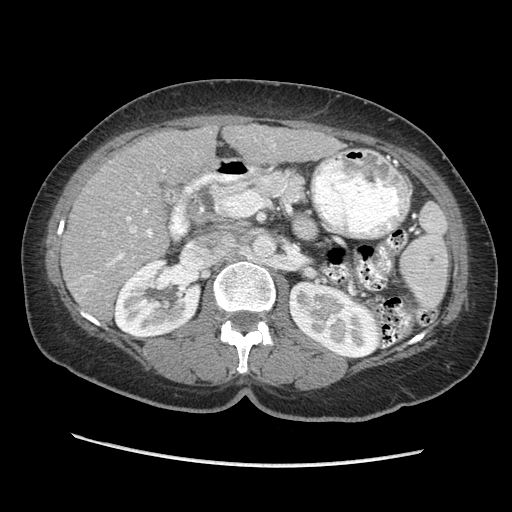
Contrast-enhanced abdominal CT (liver protocol), one axial slice; position 118 of 170 along the scan axis; reconstruction kernel STANDARD; soft-tissue window (W 400 / L 40 HU); 512 × 512 image matrix. From the clinical record (not read from this slice): diagnosis: hepatocellular carcinoma (patient treated with transarterial chemoembolisation; whether this scan precedes or follows treatment is not stated here); TNM stage (as recorded): Stage-II; Child-Pugh class: A; tumour differentiation: no biopsy; tumour nodularity: multinodular.
Outlined on this slice (semi-automatic segmentation, software-assisted and operator-edited):
- liver parenchyma outside the tumour (the mass and vessels are separate outlines, so this box may not span the whole liver): bounding box (x1, y1, x2, y2) in pixels: (62, 124, 342, 320)
- liver vessels: (82, 145, 275, 292)